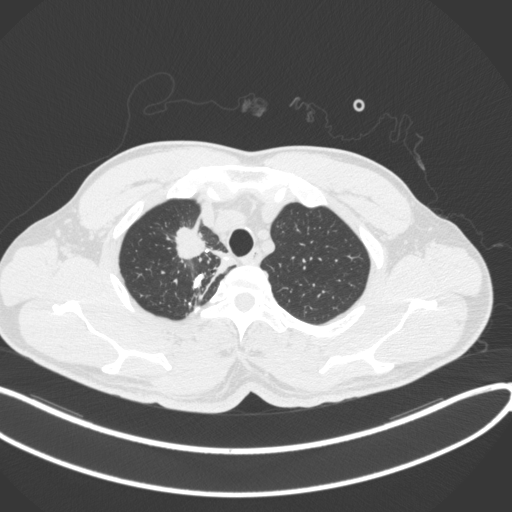
Chest CT, one axial slice; slice 322 of 391 in the series (ordered by position); 120 kVp; lung window (W 1500 / L -600 HU); 1 mm slice thickness; 512 × 512 image matrix. Male patient, age 48 years. Case-level facts recorded for this patient, not image findings: clinical TNM (as recorded): T1c N1 M1.
Structures marked on this image (bounding box drawn by a radiologist):
- lung tumour (recorded histology: adenocarcinoma): bounding box <169,217,212,263> (left, top, right, bottom; pixels)